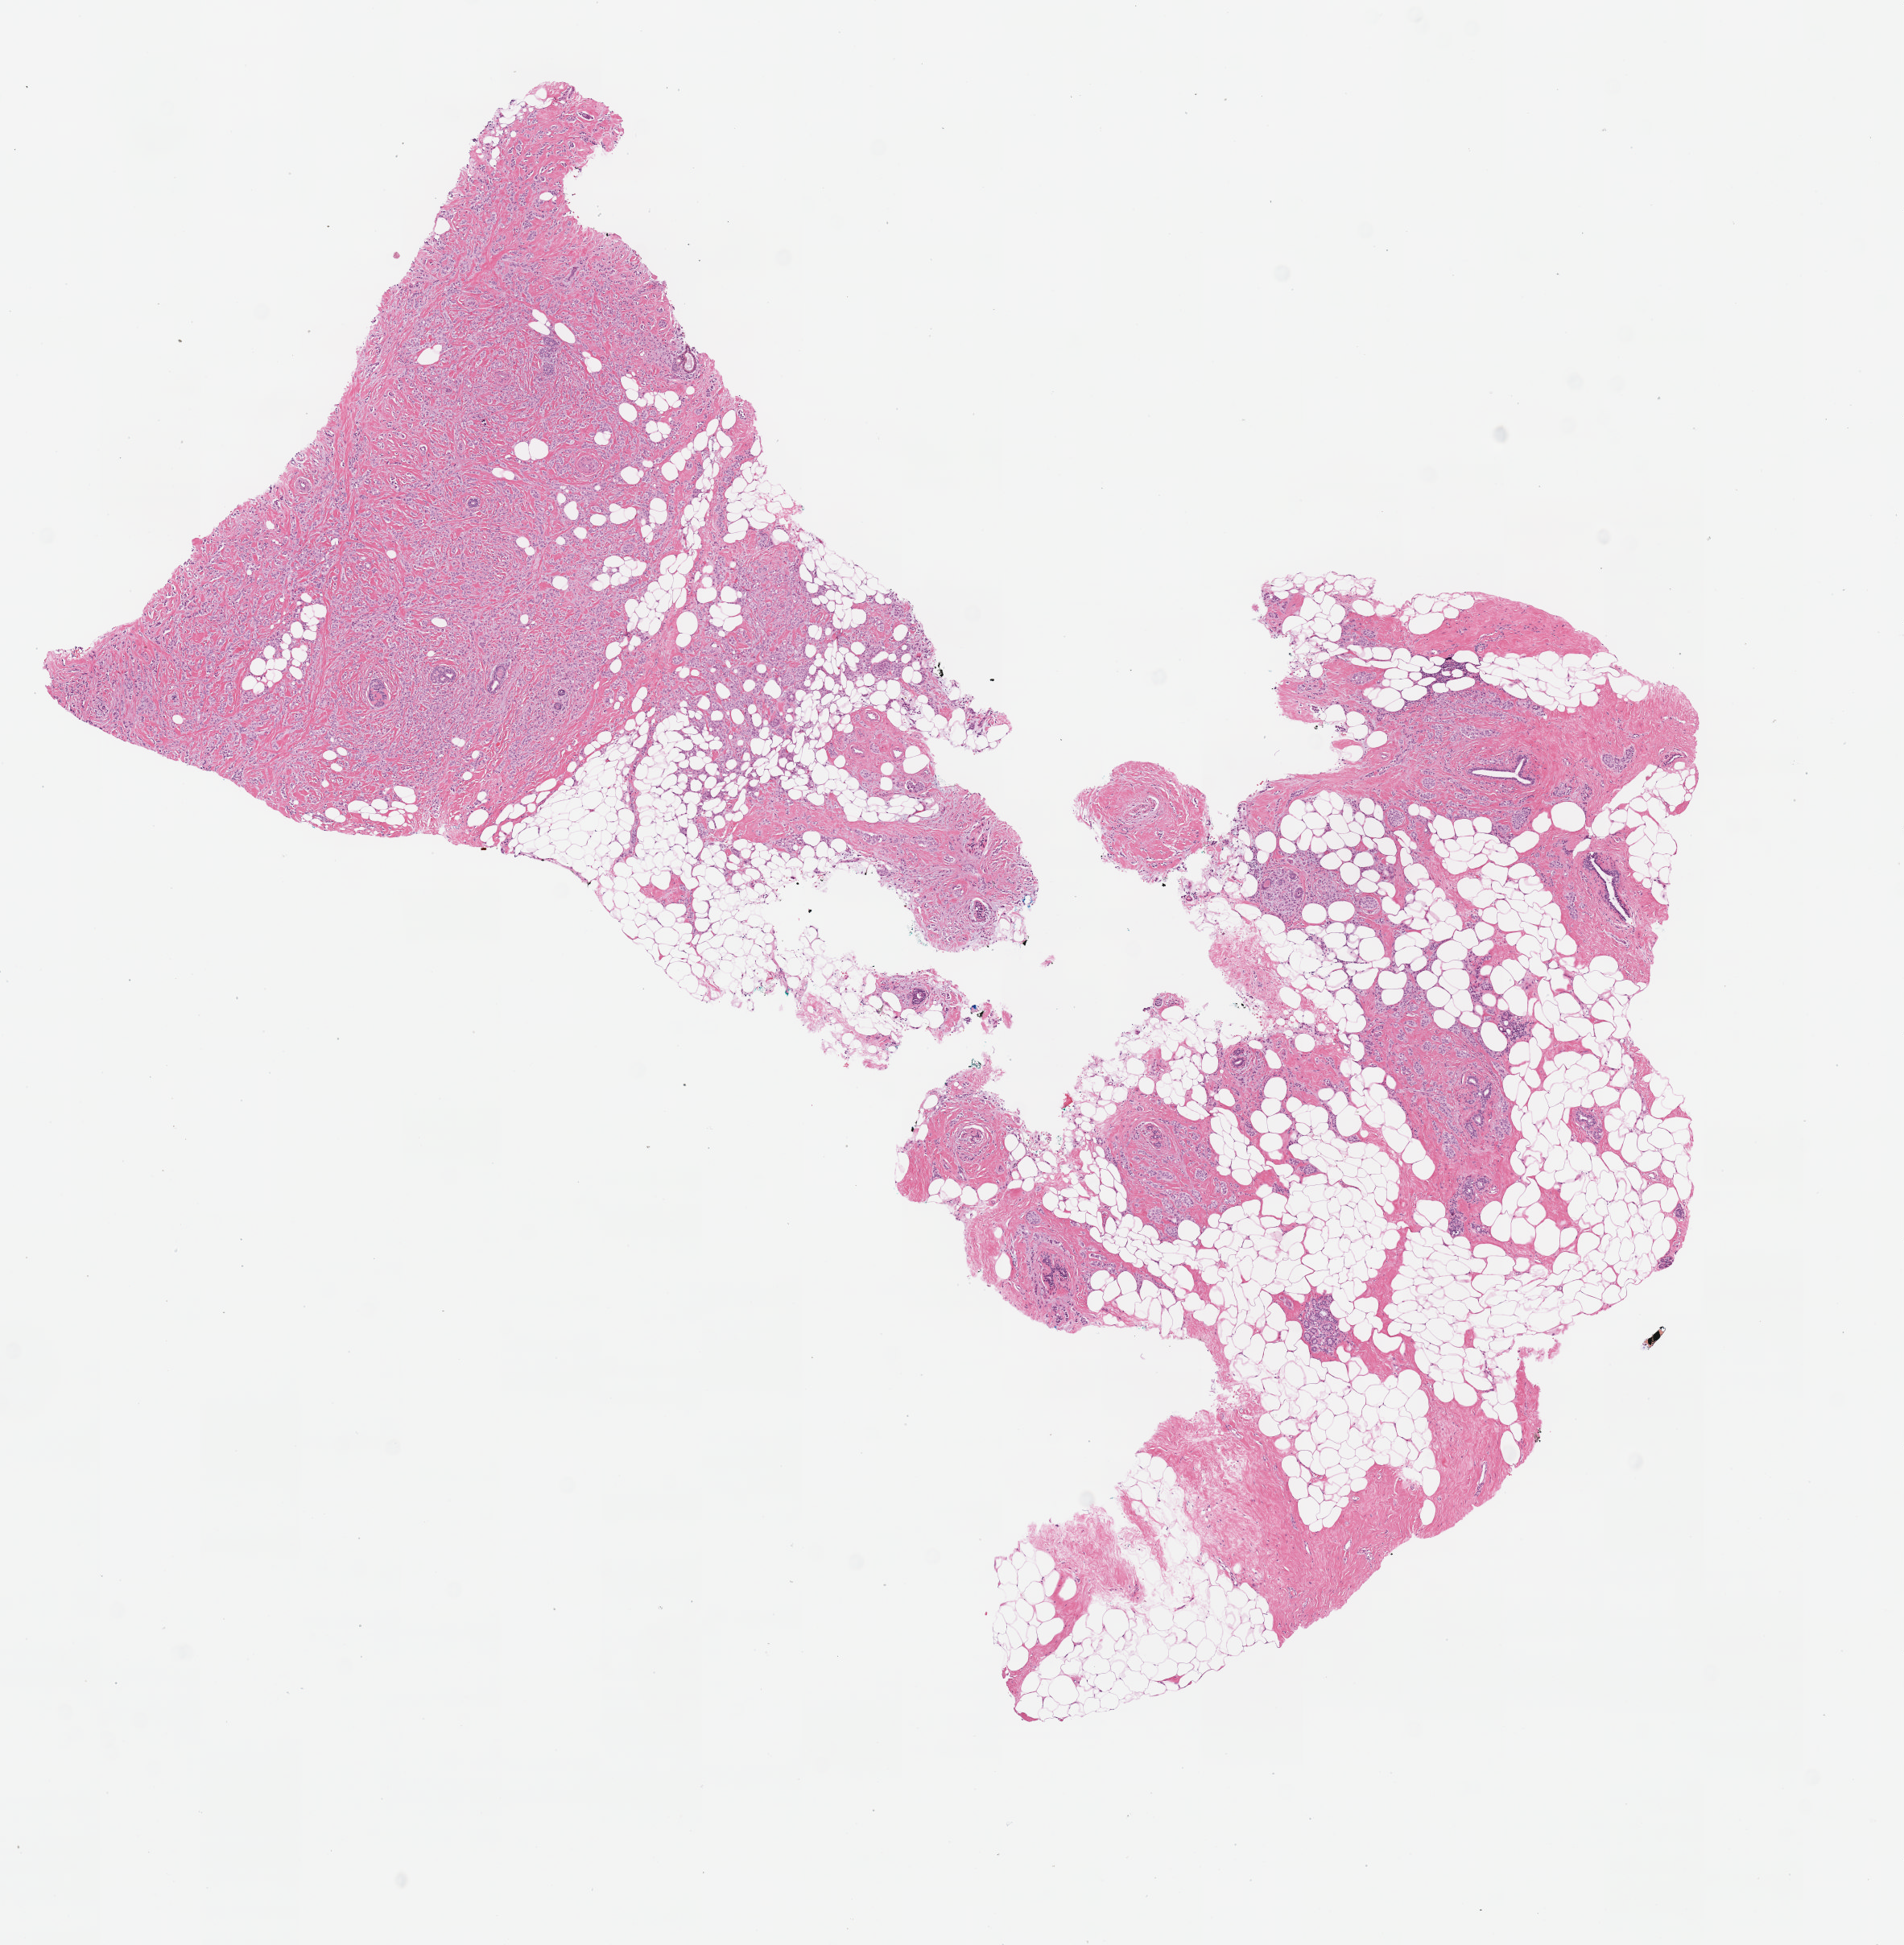
Whole-slide histology image, H&E — a low-resolution overview of the entire scanned area, about 9.3 x 9.5 mm; FFPE section; sample: primary tumour, breast. Female, age 66 years at initial diagnosis.
AJCC pathologic stage: IIB (7th edition). Lymph nodes positive (case pathology): 1 of 2 examined. Histologic diagnosis: Lobular carcinoma, NOS.